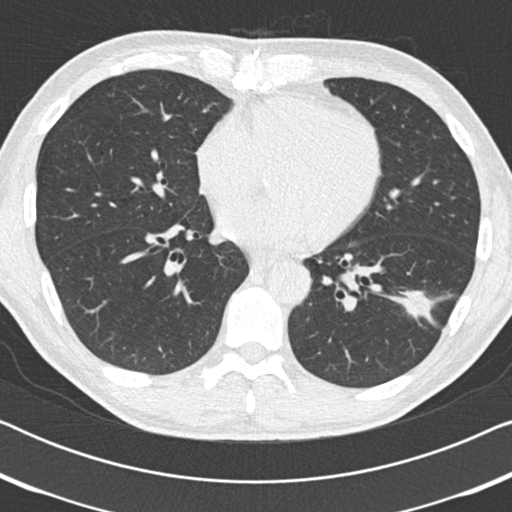
Axial slice from a low-dose chest CT screening exam, third annual screen, lung window (W 1500 / L -600 HU), 2 mm slice thickness, standard (soft-tissue) reconstruction kernel (B30f), 512 × 512 image matrix, field of view 330 × 330 mm. Male participant, aged 59 years at enrolment.
Lesion marked by an expert reader, bounding box <388,275,455,338> (left, top, right, bottom; pixels). The screening reader recorded 2 non-calcified nodules or masses ≥4 mm on this exam (left lower lobe, right middle lobe); which of them this box marks is not recorded. Later outcome: lung cancer diagnosed 73 days after this screen — adenocarcinoma, NOS, left lower lobe, poorly differentiated (G3), stage IA (AJCC 6th edition), 20 mm at pathology.